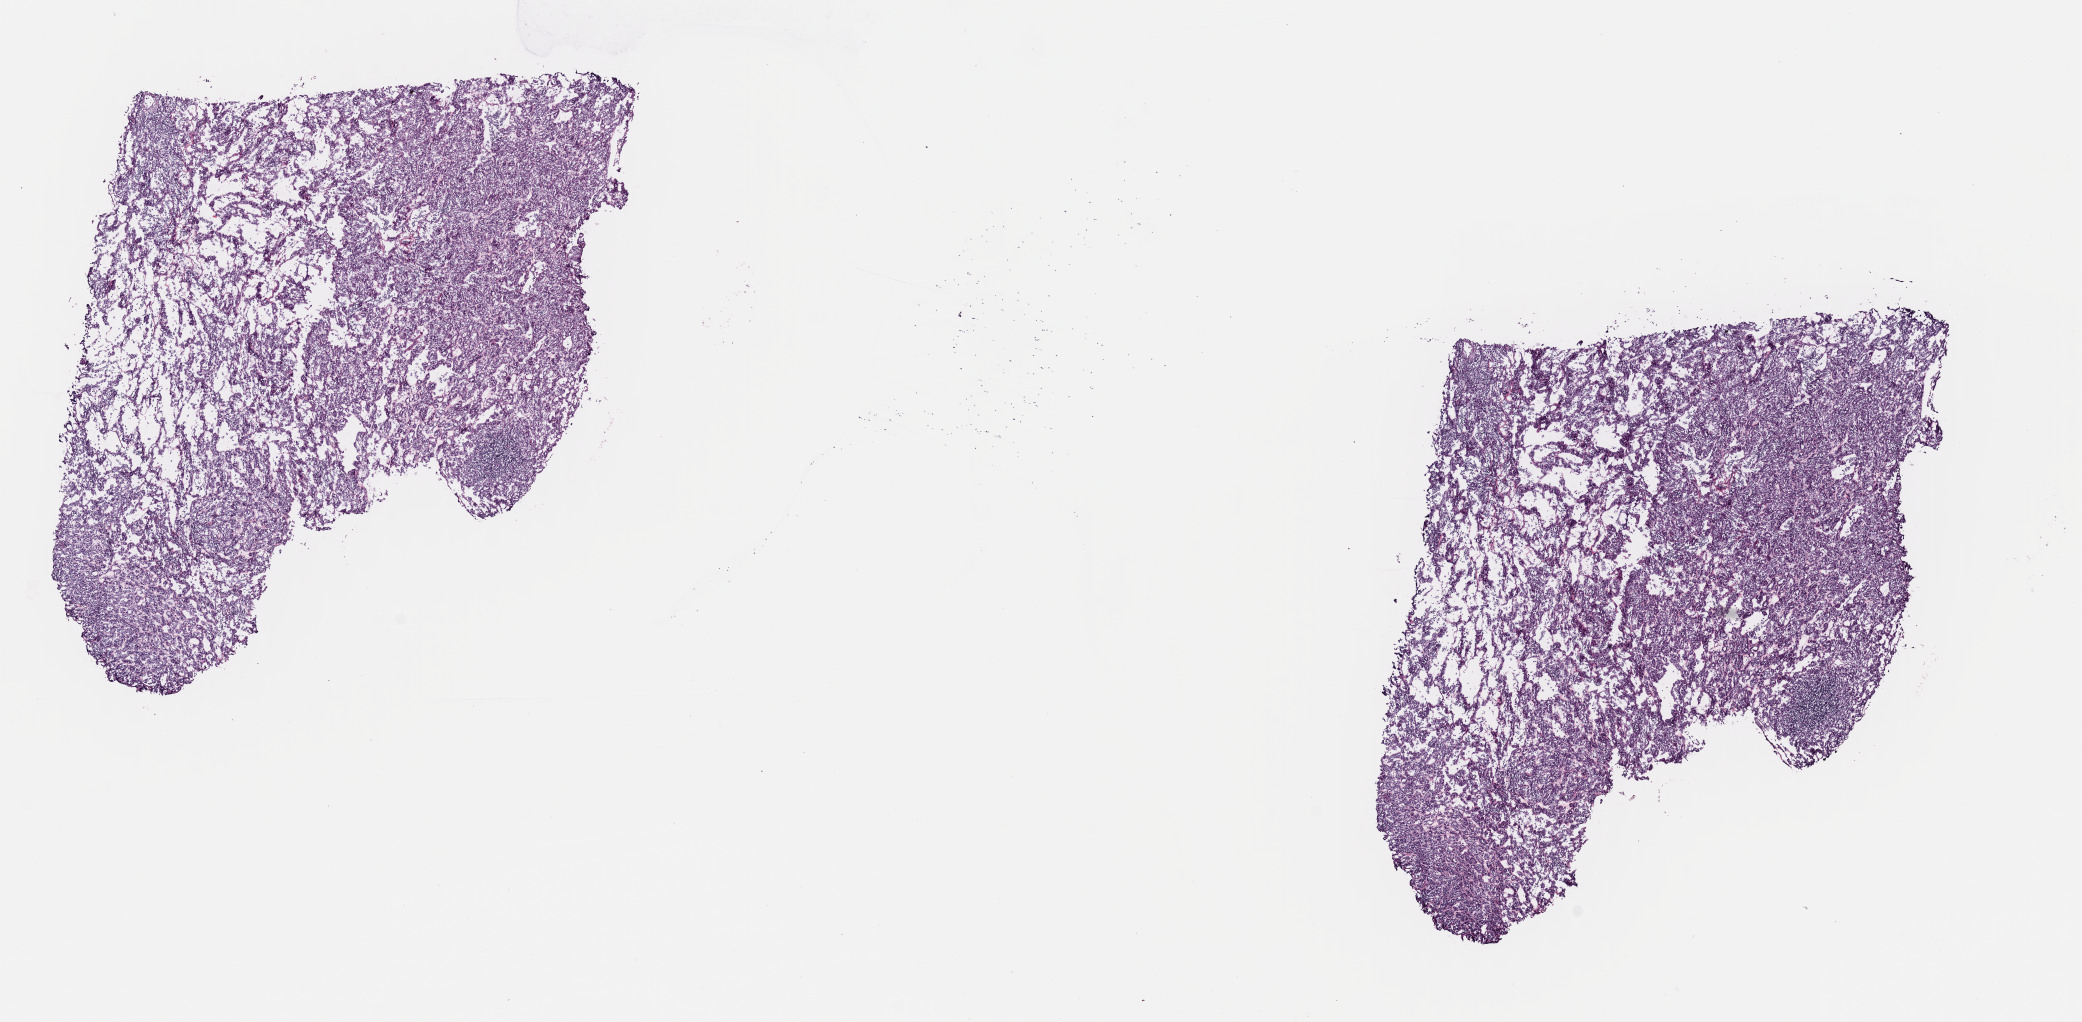
Digitized H&E-stained tissue section (whole slide), low-resolution overview of the scanned area, about 16.4 x 8.1 mm (from a 40x scan). Frozen section from the top of the tissue portion. Thyroid, primary tumour sample. Female patient; age at initial diagnosis 26 years. Slide review estimates, as recorded: tumour cells 85%, tumour nuclei 85%, normal cells 0%, stromal cells 15%, necrosis 0%. Infiltration values recorded for this section: lymphocyte infiltration 5%, monocyte infiltration 0%, neutrophil infiltration 0%.
* TNM: T2 N0 MX
* AJCC pathologic stage: I (7th edition)
* histologic diagnosis: Papillary carcinoma, follicular variant
* lymph nodes positive (case pathology): 0 of 27 examined